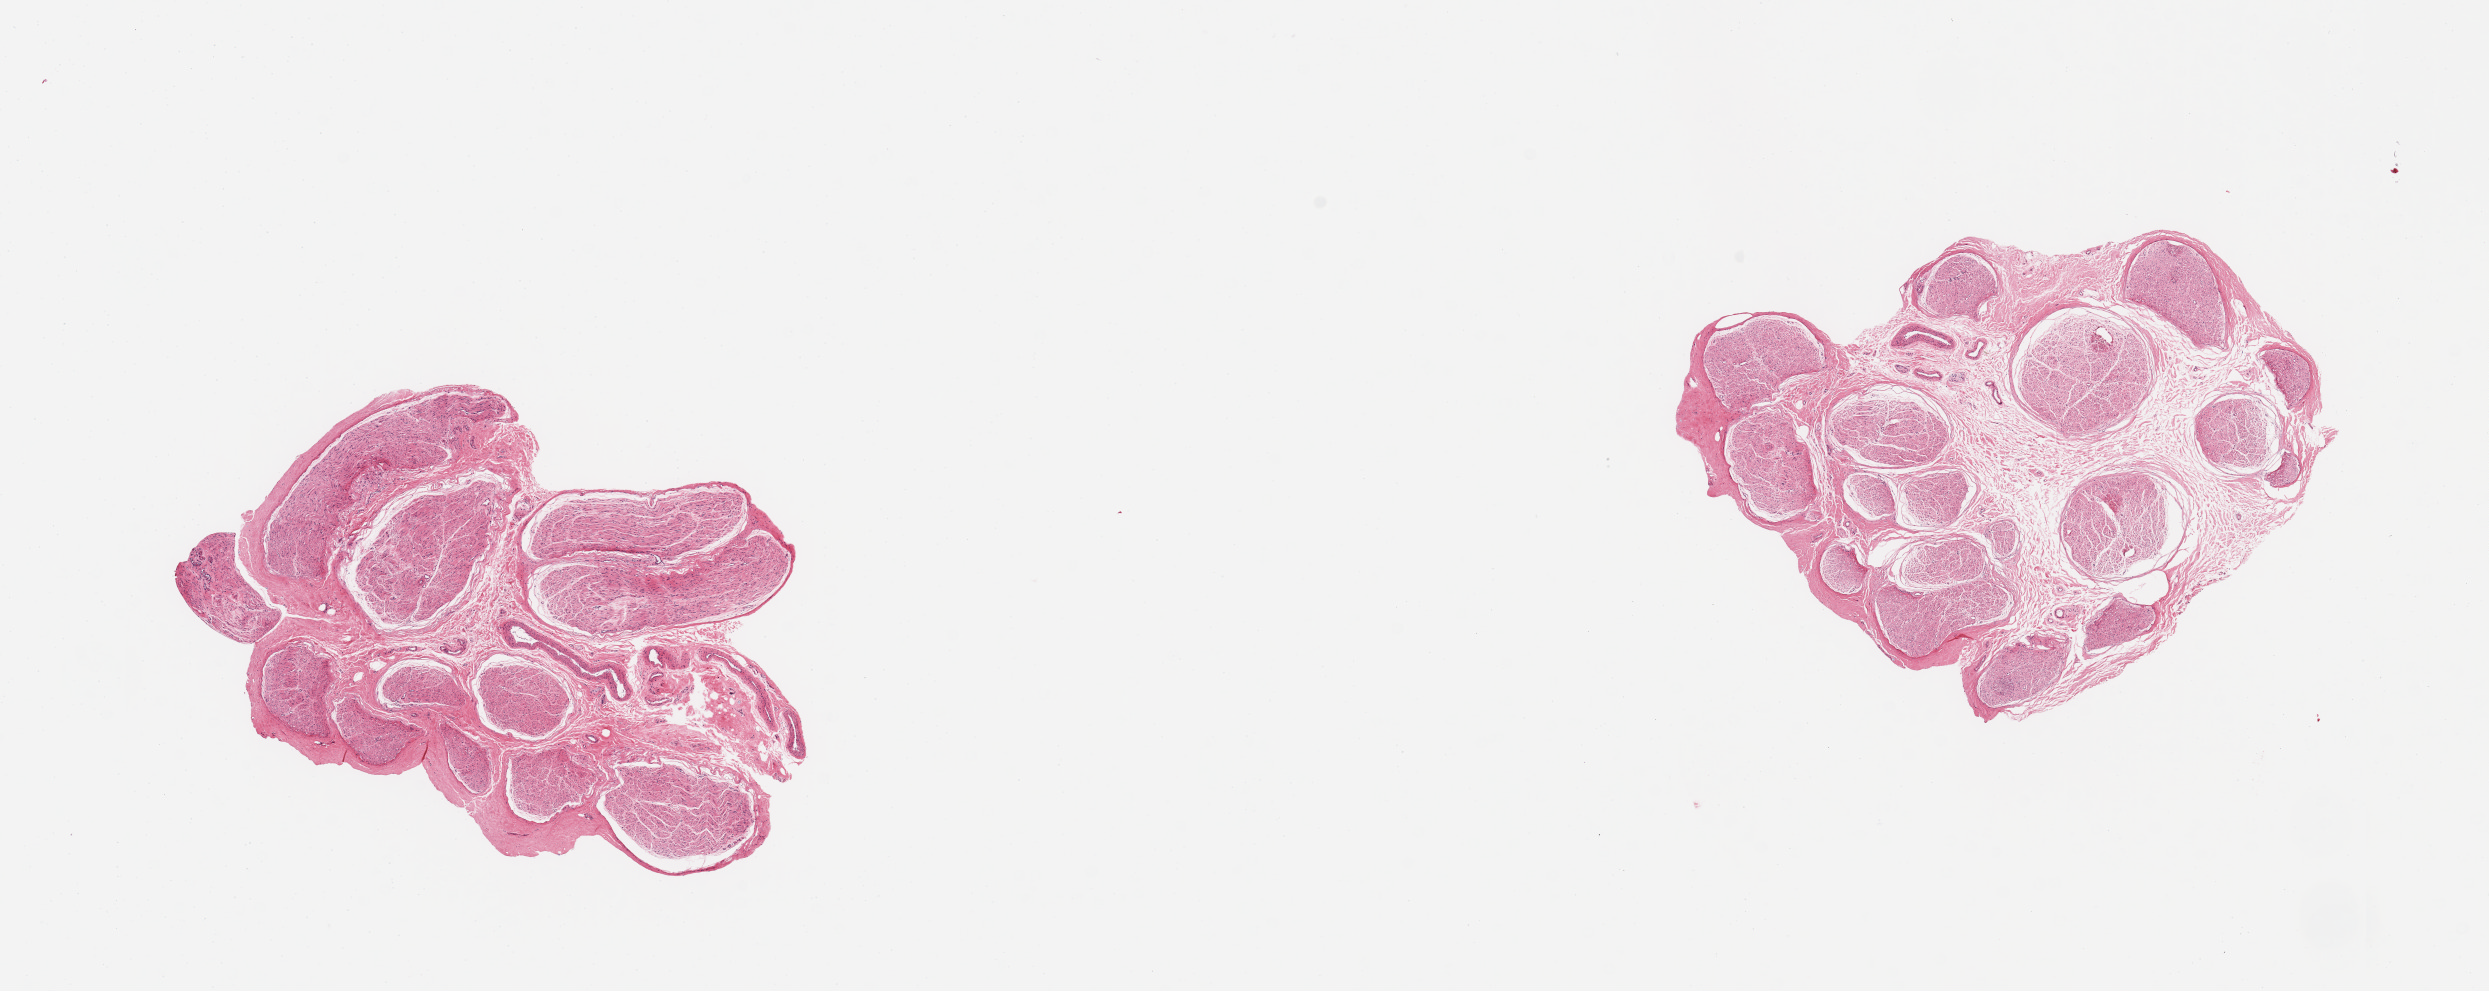
Haematoxylin and eosin whole-slide image, shown as a low-resolution overview of the whole scanned area (about 19.7 x 7.8 mm), PAXgene-fixed paraffin-embedded (PFPE) section, section of tibial nerve (target tissue), donor tissue sample. Donor sex: male.
Pathologist's review note for this sample: 2 pieces, no adherent fat.